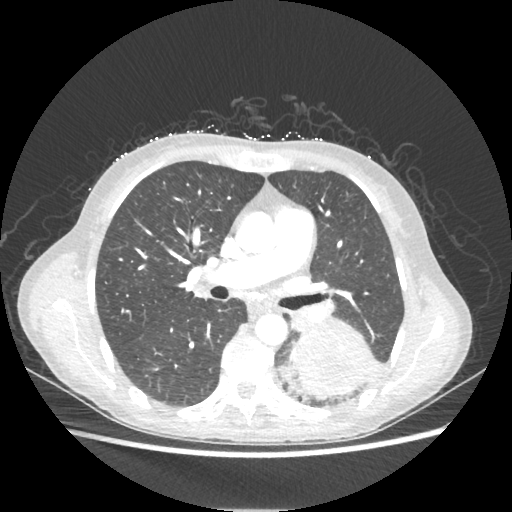
Chest CT, one axial slice; slice 125 of 221 in the series (ordered by position); reconstruction kernel STANDARD; lung window (W 1500 / L -600 HU); 1.25 mm slice thickness; 512 × 512 image matrix. Patient: female, 53 years. From the clinical record (not read from this slice): clinical TNM (as recorded): T3 N0 M0.
Annotated regions visible in this slice (bounding box drawn by a radiologist):
- lung tumour (recorded histology: adenocarcinoma): bounding box [x1, y1, x2, y2] px = [292, 324, 374, 398]